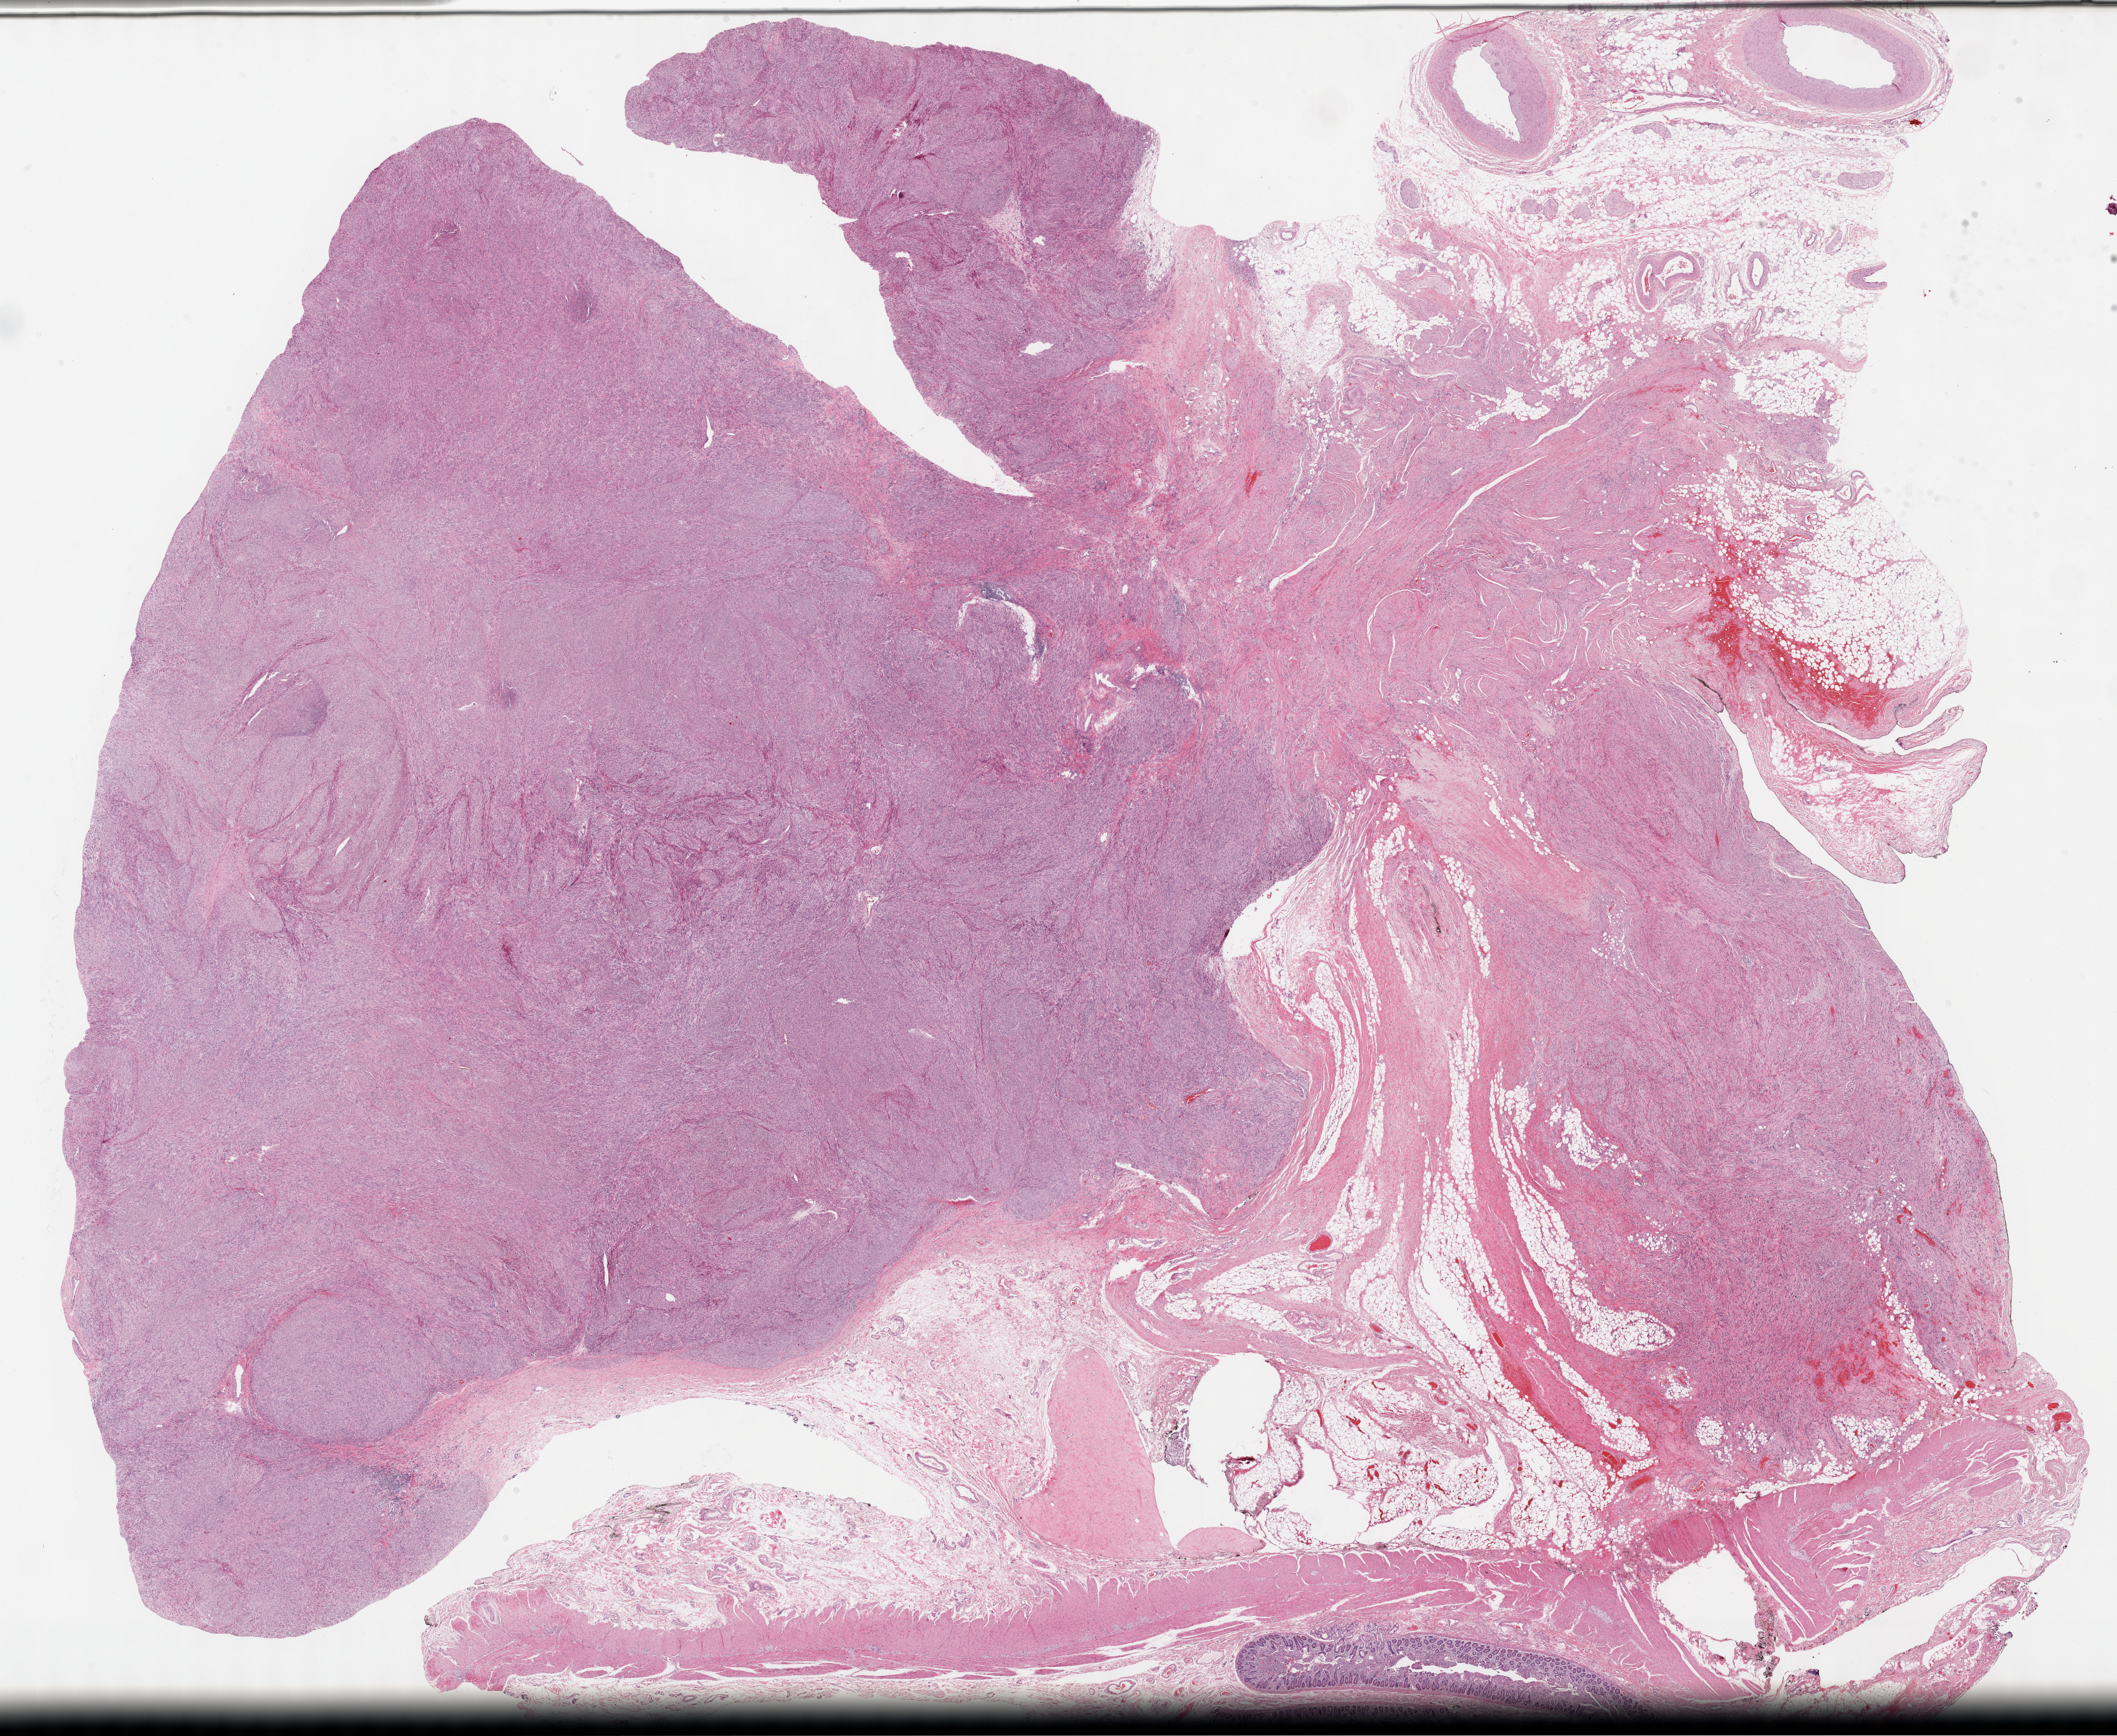
Whole-slide histology image, Hematoxylin and eosin (H&E) stained — a low-resolution overview of the entire scanned area, about 29.2 x 23.9 mm (acquisition: 40x scan); FFPE section; primary tumour sample from the retroperitoneum and peritoneum. Patient: female, age at initial diagnosis 78 years.
Pathologic diagnosis: Dedifferentiated liposarcoma (retroperitoneum).